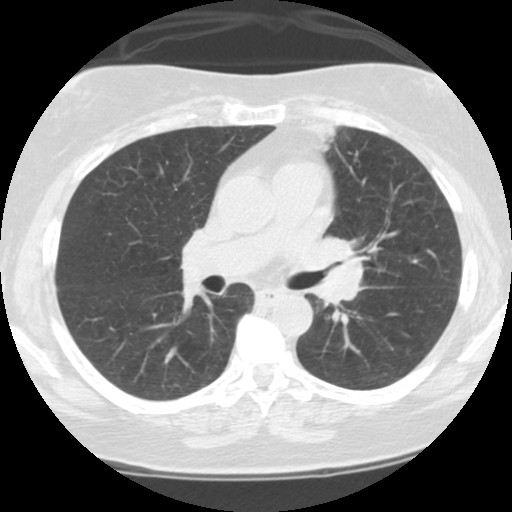
Low-dose screening chest CT, one axial slice. Slice 63 of 108 in the series (ordered by position). Reconstruction kernel STANDARD. Lung window (W 1500 / L -600 HU). 2.5 mm slice thickness. 512 × 512 image matrix.
Outlined on this slice (manually delineated by an expert):
- lesion 1 (tumor, hilum of left lung): bounding box [x1, y1, x2, y2] px = [307, 235, 365, 306]